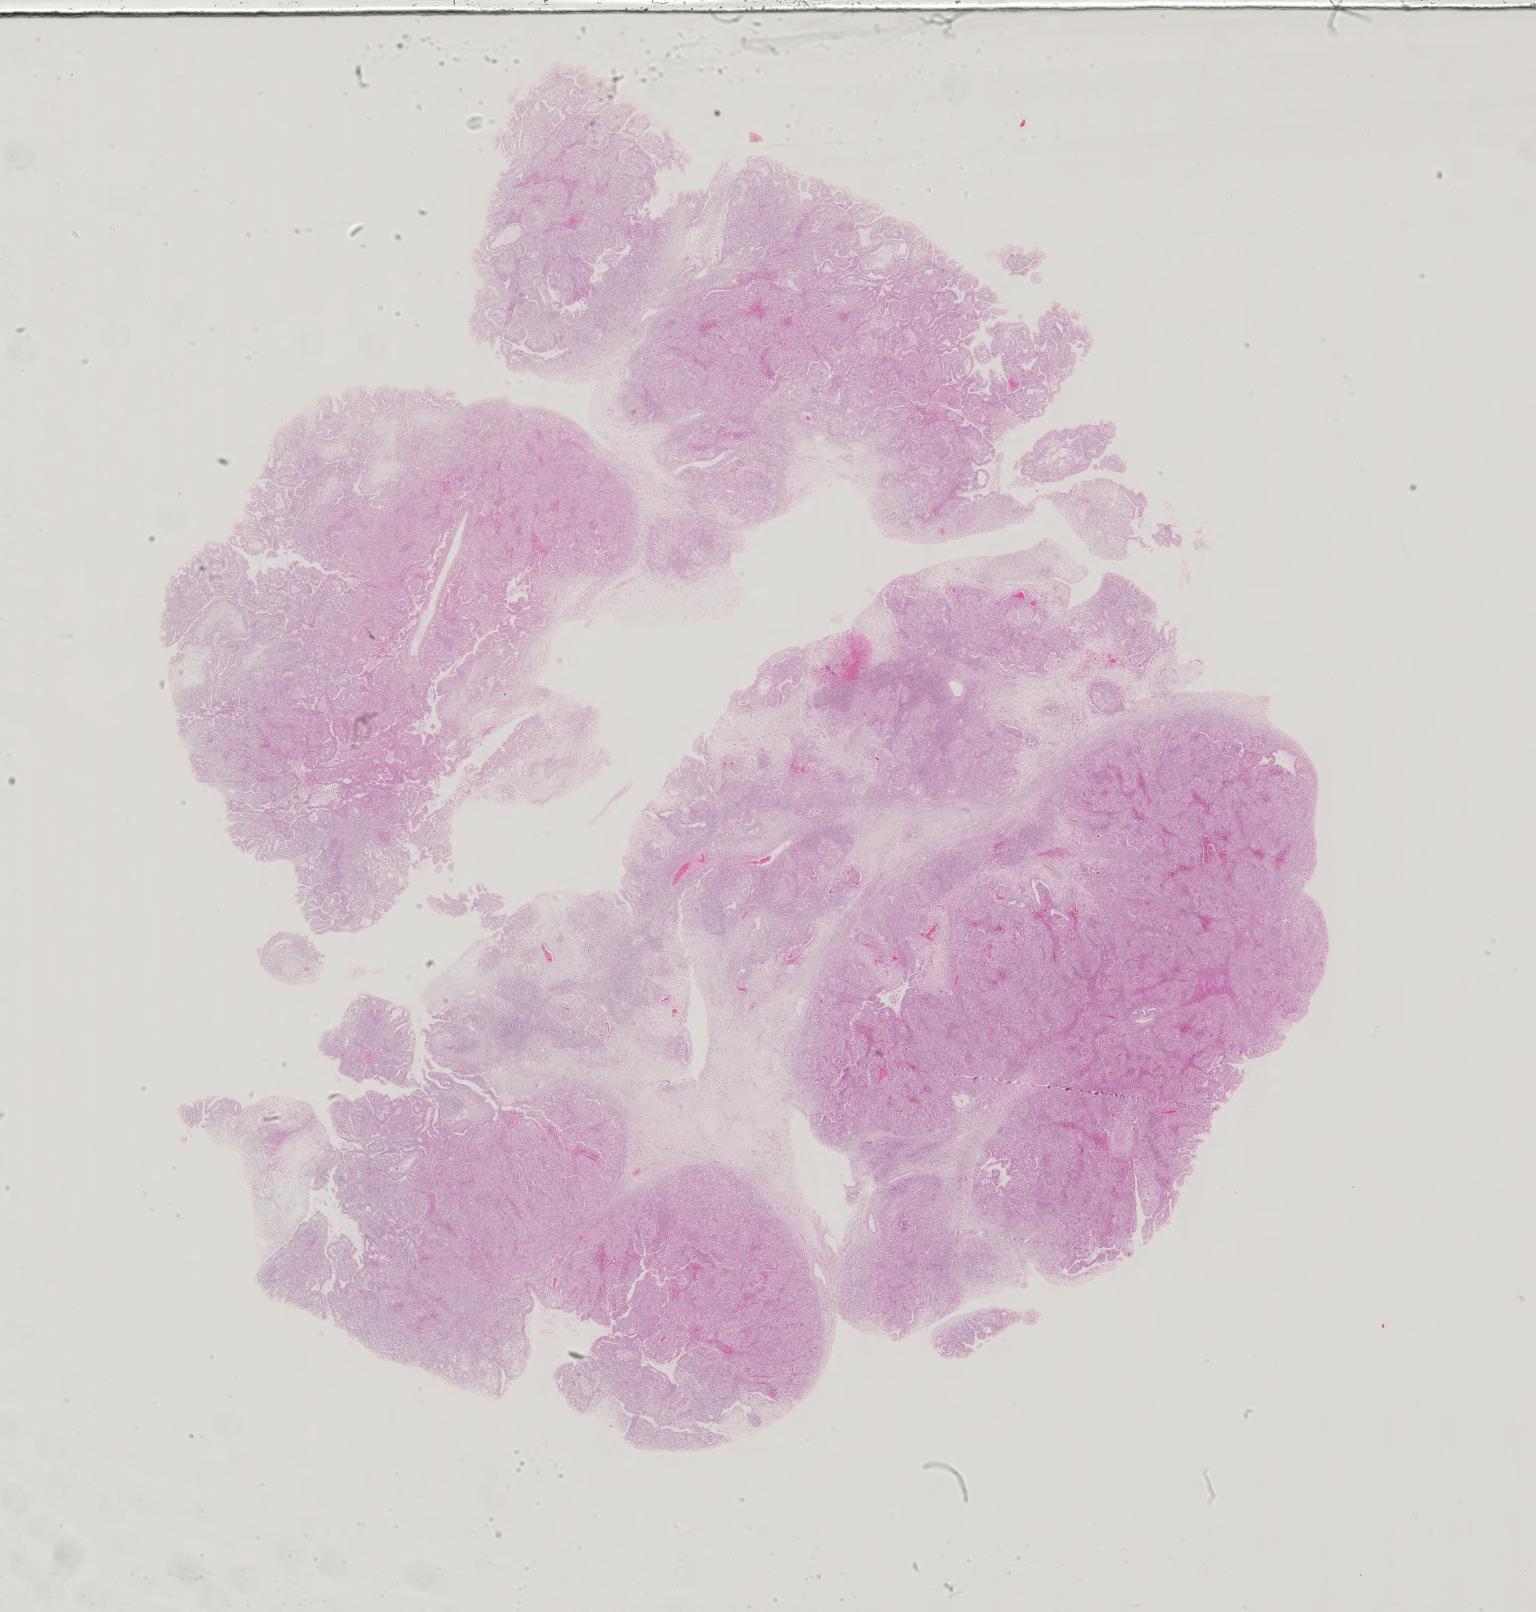
Digitized H&E tissue section (whole slide), whole scanned area (about 22.4 x 23.5 mm, acquisition: 40x scan) shown as a low-resolution overview. Male patient.
Specimen: formalin-fixed paraffin-embedded (FFPE) diagnostic section; testis, primary tumour sample.